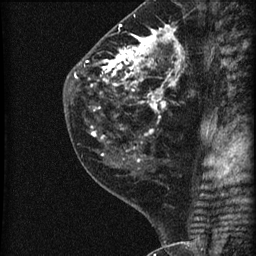
Breast MRI (dynamic contrast-enhanced), one sagittal slice; position 27 of 60 along the scan axis; dynamic contrast-enhanced series, image 2 of 3 at this slice position (ordered by acquisition); 1.5 T; TE 4.2 ms, TR 22.7 ms; 1.8 mm slice thickness; 256 × 256 image matrix, field of view 180 × 180 mm. Patient: female, 45 years. Case-level facts recorded for this patient, not image findings: setting: breast cancer imaged before/during neoadjuvant chemotherapy; receptor status: HR-positive, HER2-negative.
Annotated regions visible in this slice (semi-automatic segmentation, software-assisted and operator-edited):
- analysis volume of interest (the breast-tissue region the enhancement analysis was run in; not a lesion): bounding box <74,11,205,140> (left, top, right, bottom; pixels)
- tumour enhancement mask (voxels above the 90 % enhancement threshold inside the analysis volume of interest): <87,25,183,136>